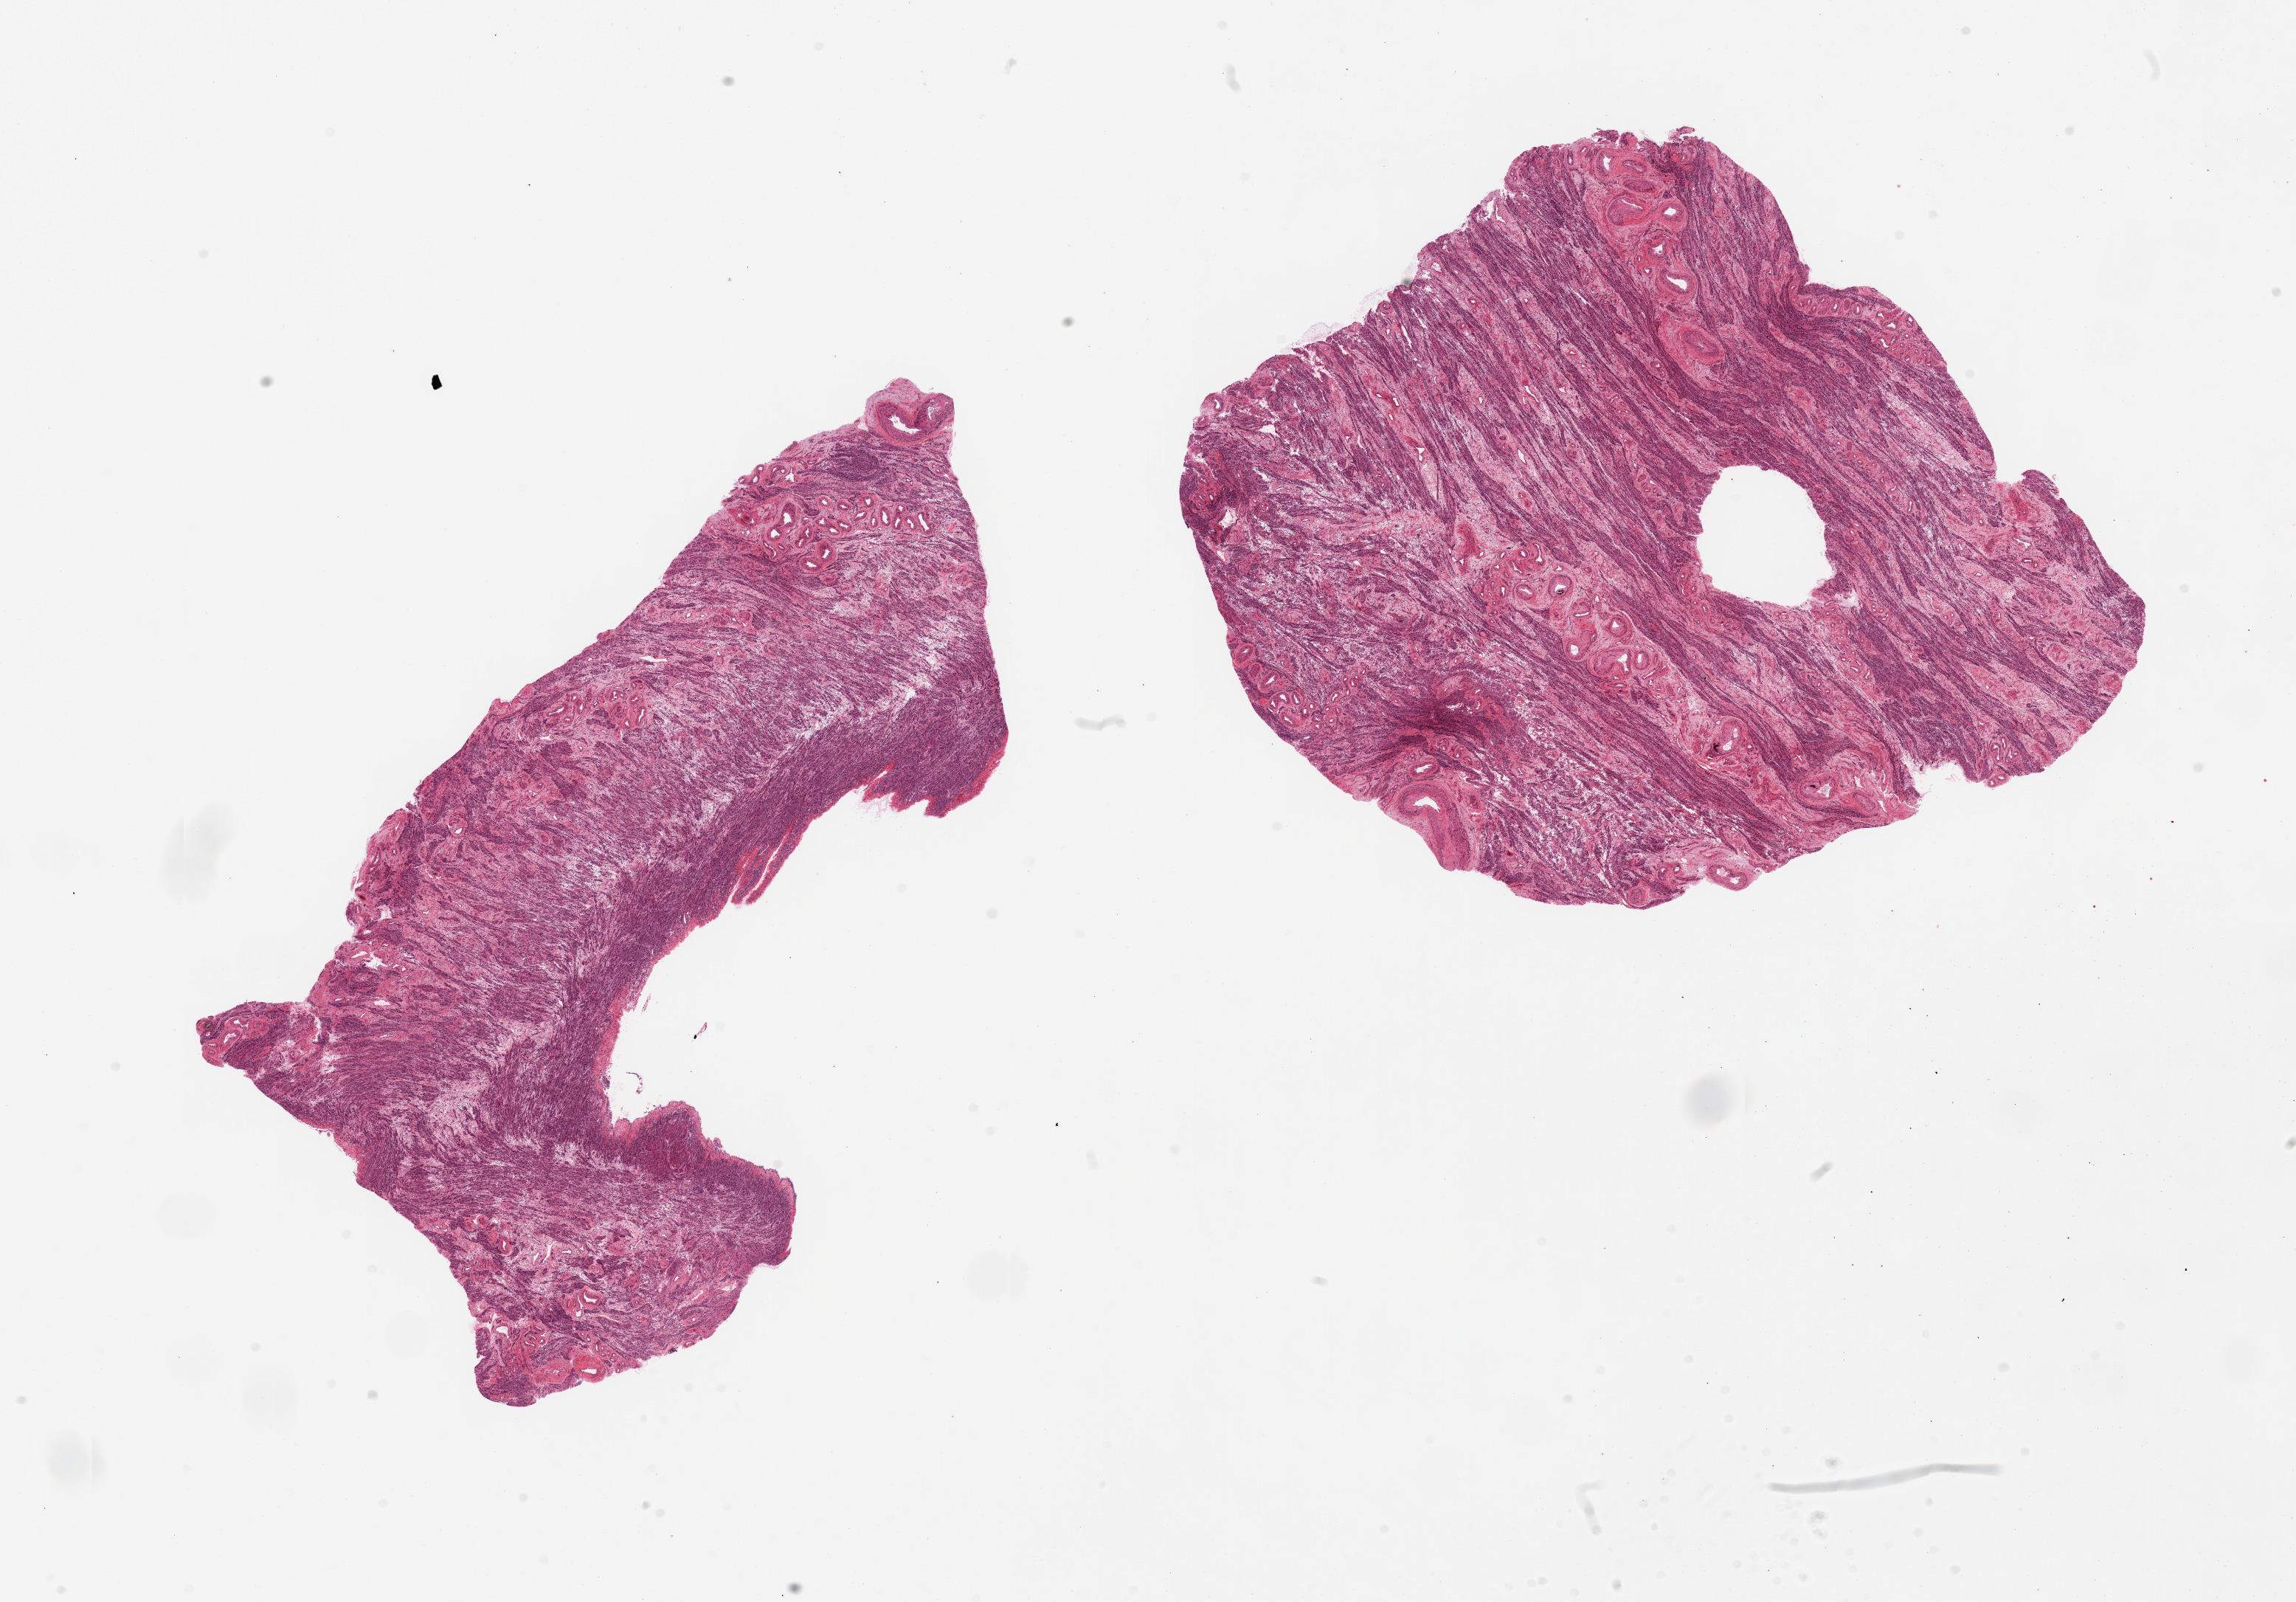
Digitized H&E-stained section, brightfield — whole scanned area (about 24.6 x 17.2 mm) shown as a low-resolution overview; PAXgene-fixed, paraffin-embedded tissue; target tissue: uterus; tissue donor sample. Female donor.
- pathologist's review note for this sample: 2 pieces, myometrium, some vascular calcification